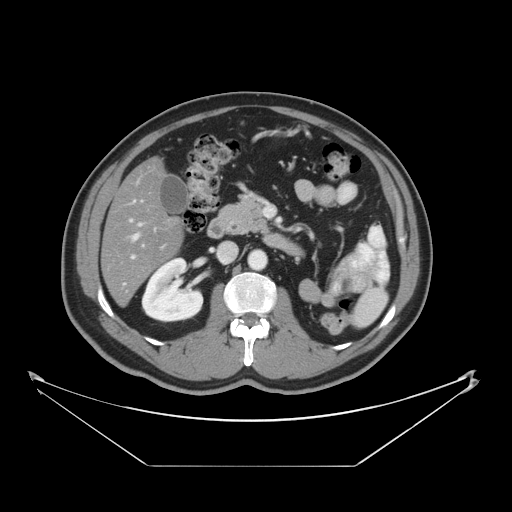
Contrast-enhanced abdominal CT, one axial slice; reconstruction kernel STANDARD; 120 kVp; intravenous contrast given; soft-tissue window (W 400 / L 40 HU); 5 mm slice thickness; 512 × 512 image matrix, field of view 465 × 465 mm. Male patient, age 57 years. Case-level facts recorded for this patient, not image findings: diagnosis: colorectal cancer liver metastases, imaged before liver resection; multiple liver metastases: no; largest metastasis: 3.3 cm; disease in both lobes: no.
Annotated regions visible in this slice (outlined manually by an expert reader):
- hepatic veins: bounding box <130,219,142,240> (left, top, right, bottom; pixels)
- liver: <104,159,183,304>
- planned liver remnant (the part of the liver to remain after resection): <104,159,182,303>
- portal vein (with intrahepatic branches): <132,255,135,259>